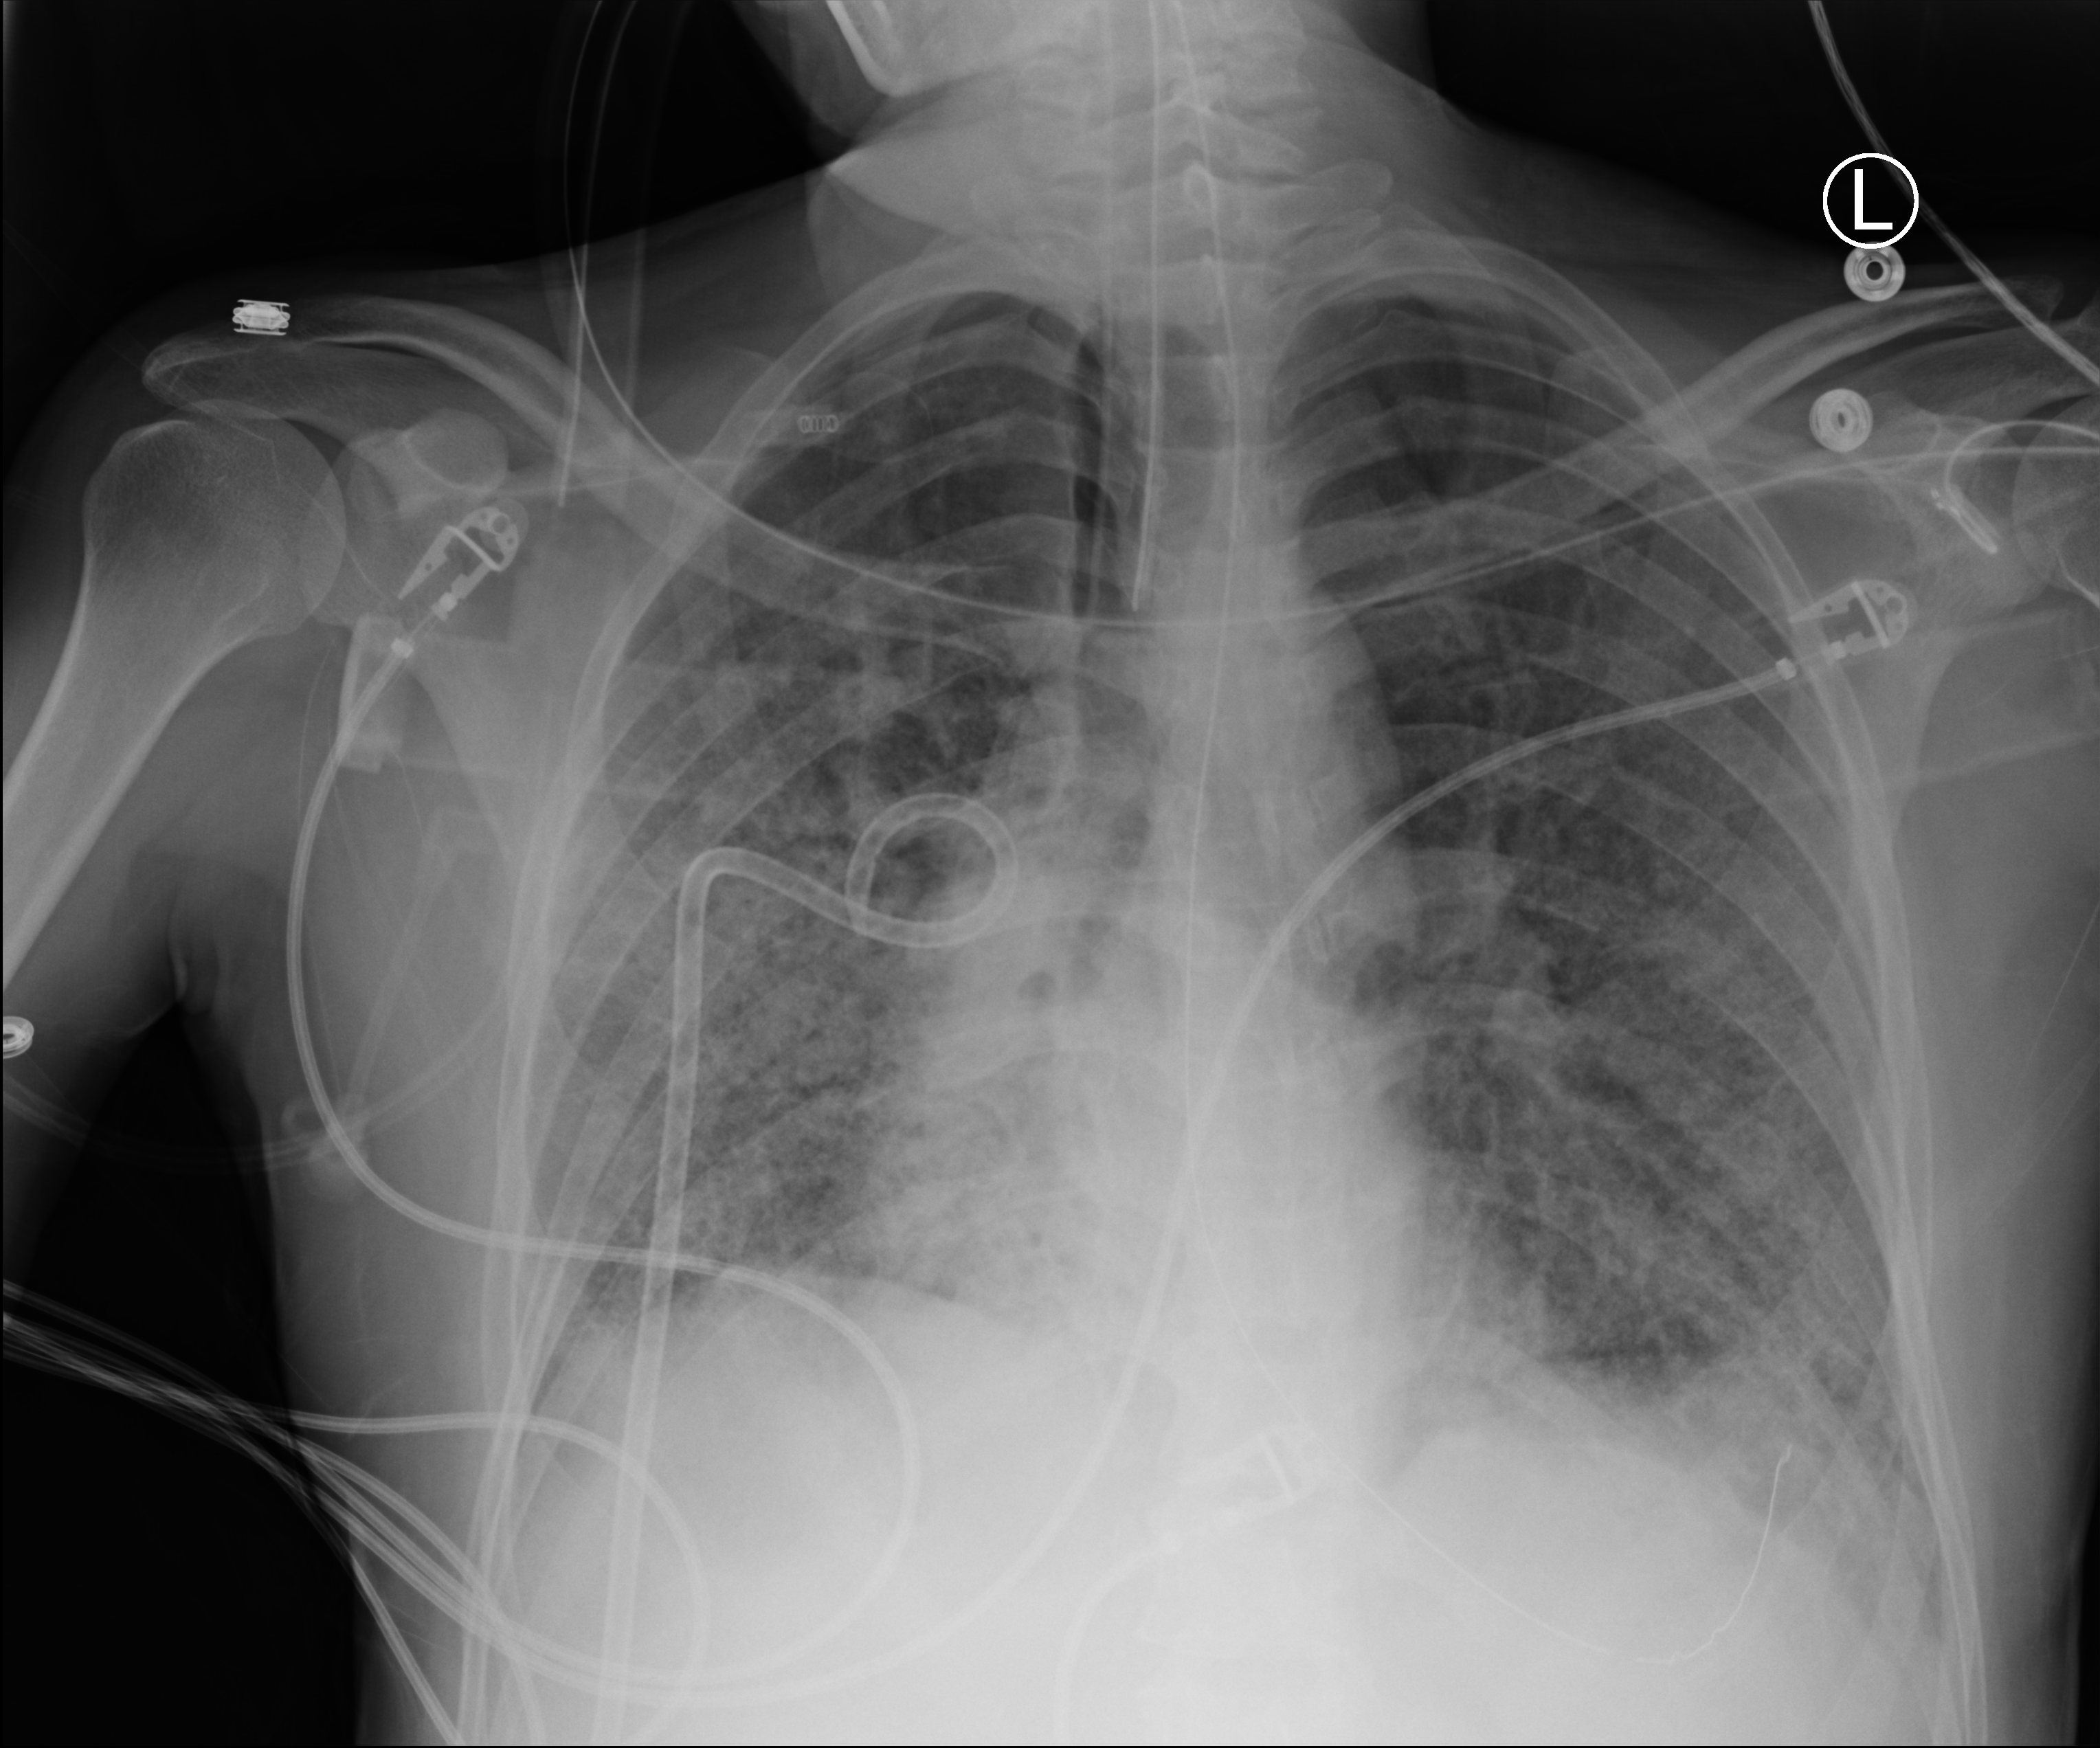
Bedside chest radiograph (computed radiography); anteroposterior (AP) projection. Patient hospitalised with COVID-19, aged 18–59 years.
Admission-level facts for this patient (not findings on this image; timing relative to this image not recorded): chronic kidney disease (admission record): no; smoking status (admission record): never; COPD (admission record): no.